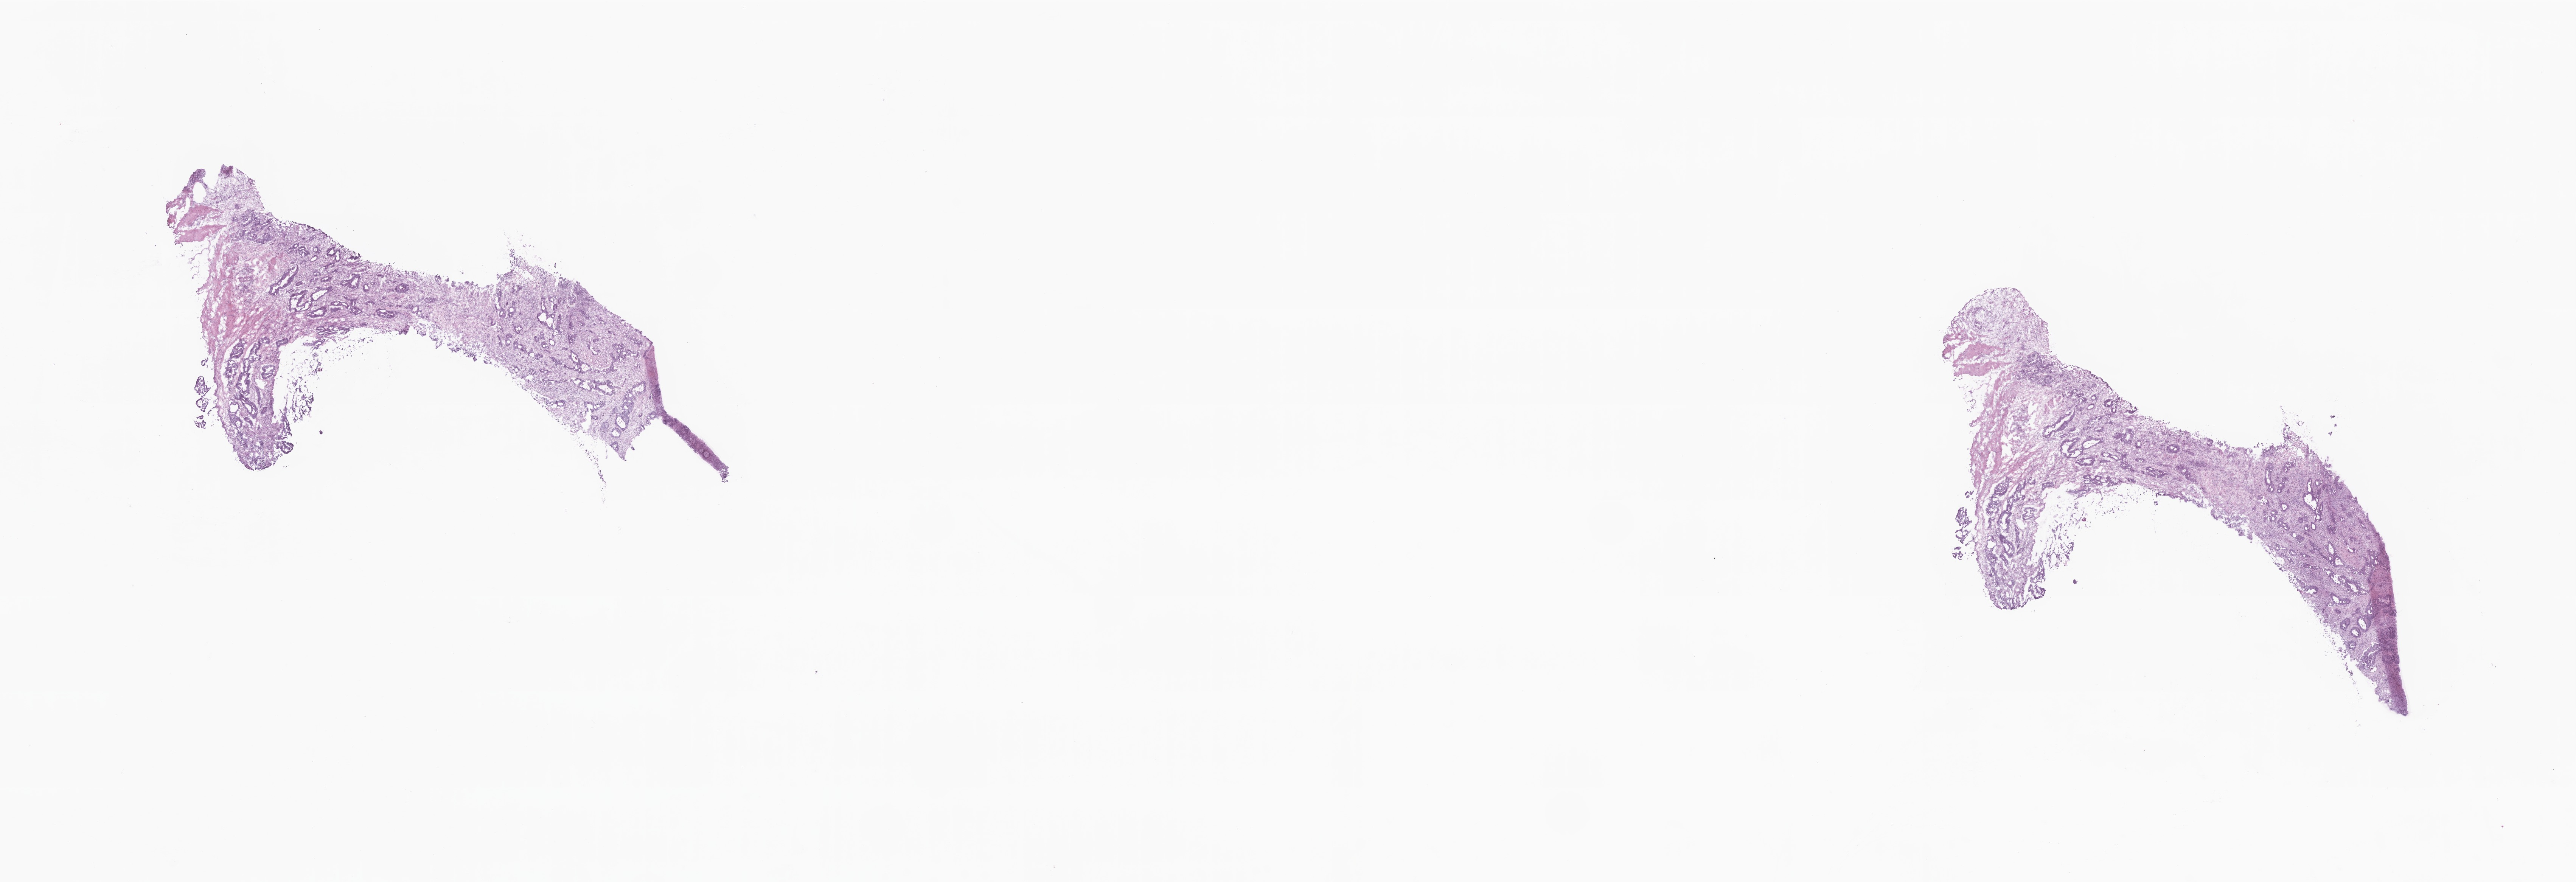
H&E whole-slide image — a low-resolution overview of the entire scanned area, about 28.7 x 9.8 mm; cryosection; primary tumor; anatomic site: sigmoid colon. Patient: male, age at initial diagnosis 75 years. Composition of this section per pathologist review: tumor cells 55%, tumor nuclei 90%, stromal cells 45%, necrosis 0%, normal cells 0%. Infiltration values recorded for this section: lymphocyte infiltration 0%, monocyte infiltration 0%, neutrophil infiltration 0%.
Section: bottom of the tissue portion. Histologic diagnosis: Adenocarcinoma, NOS.